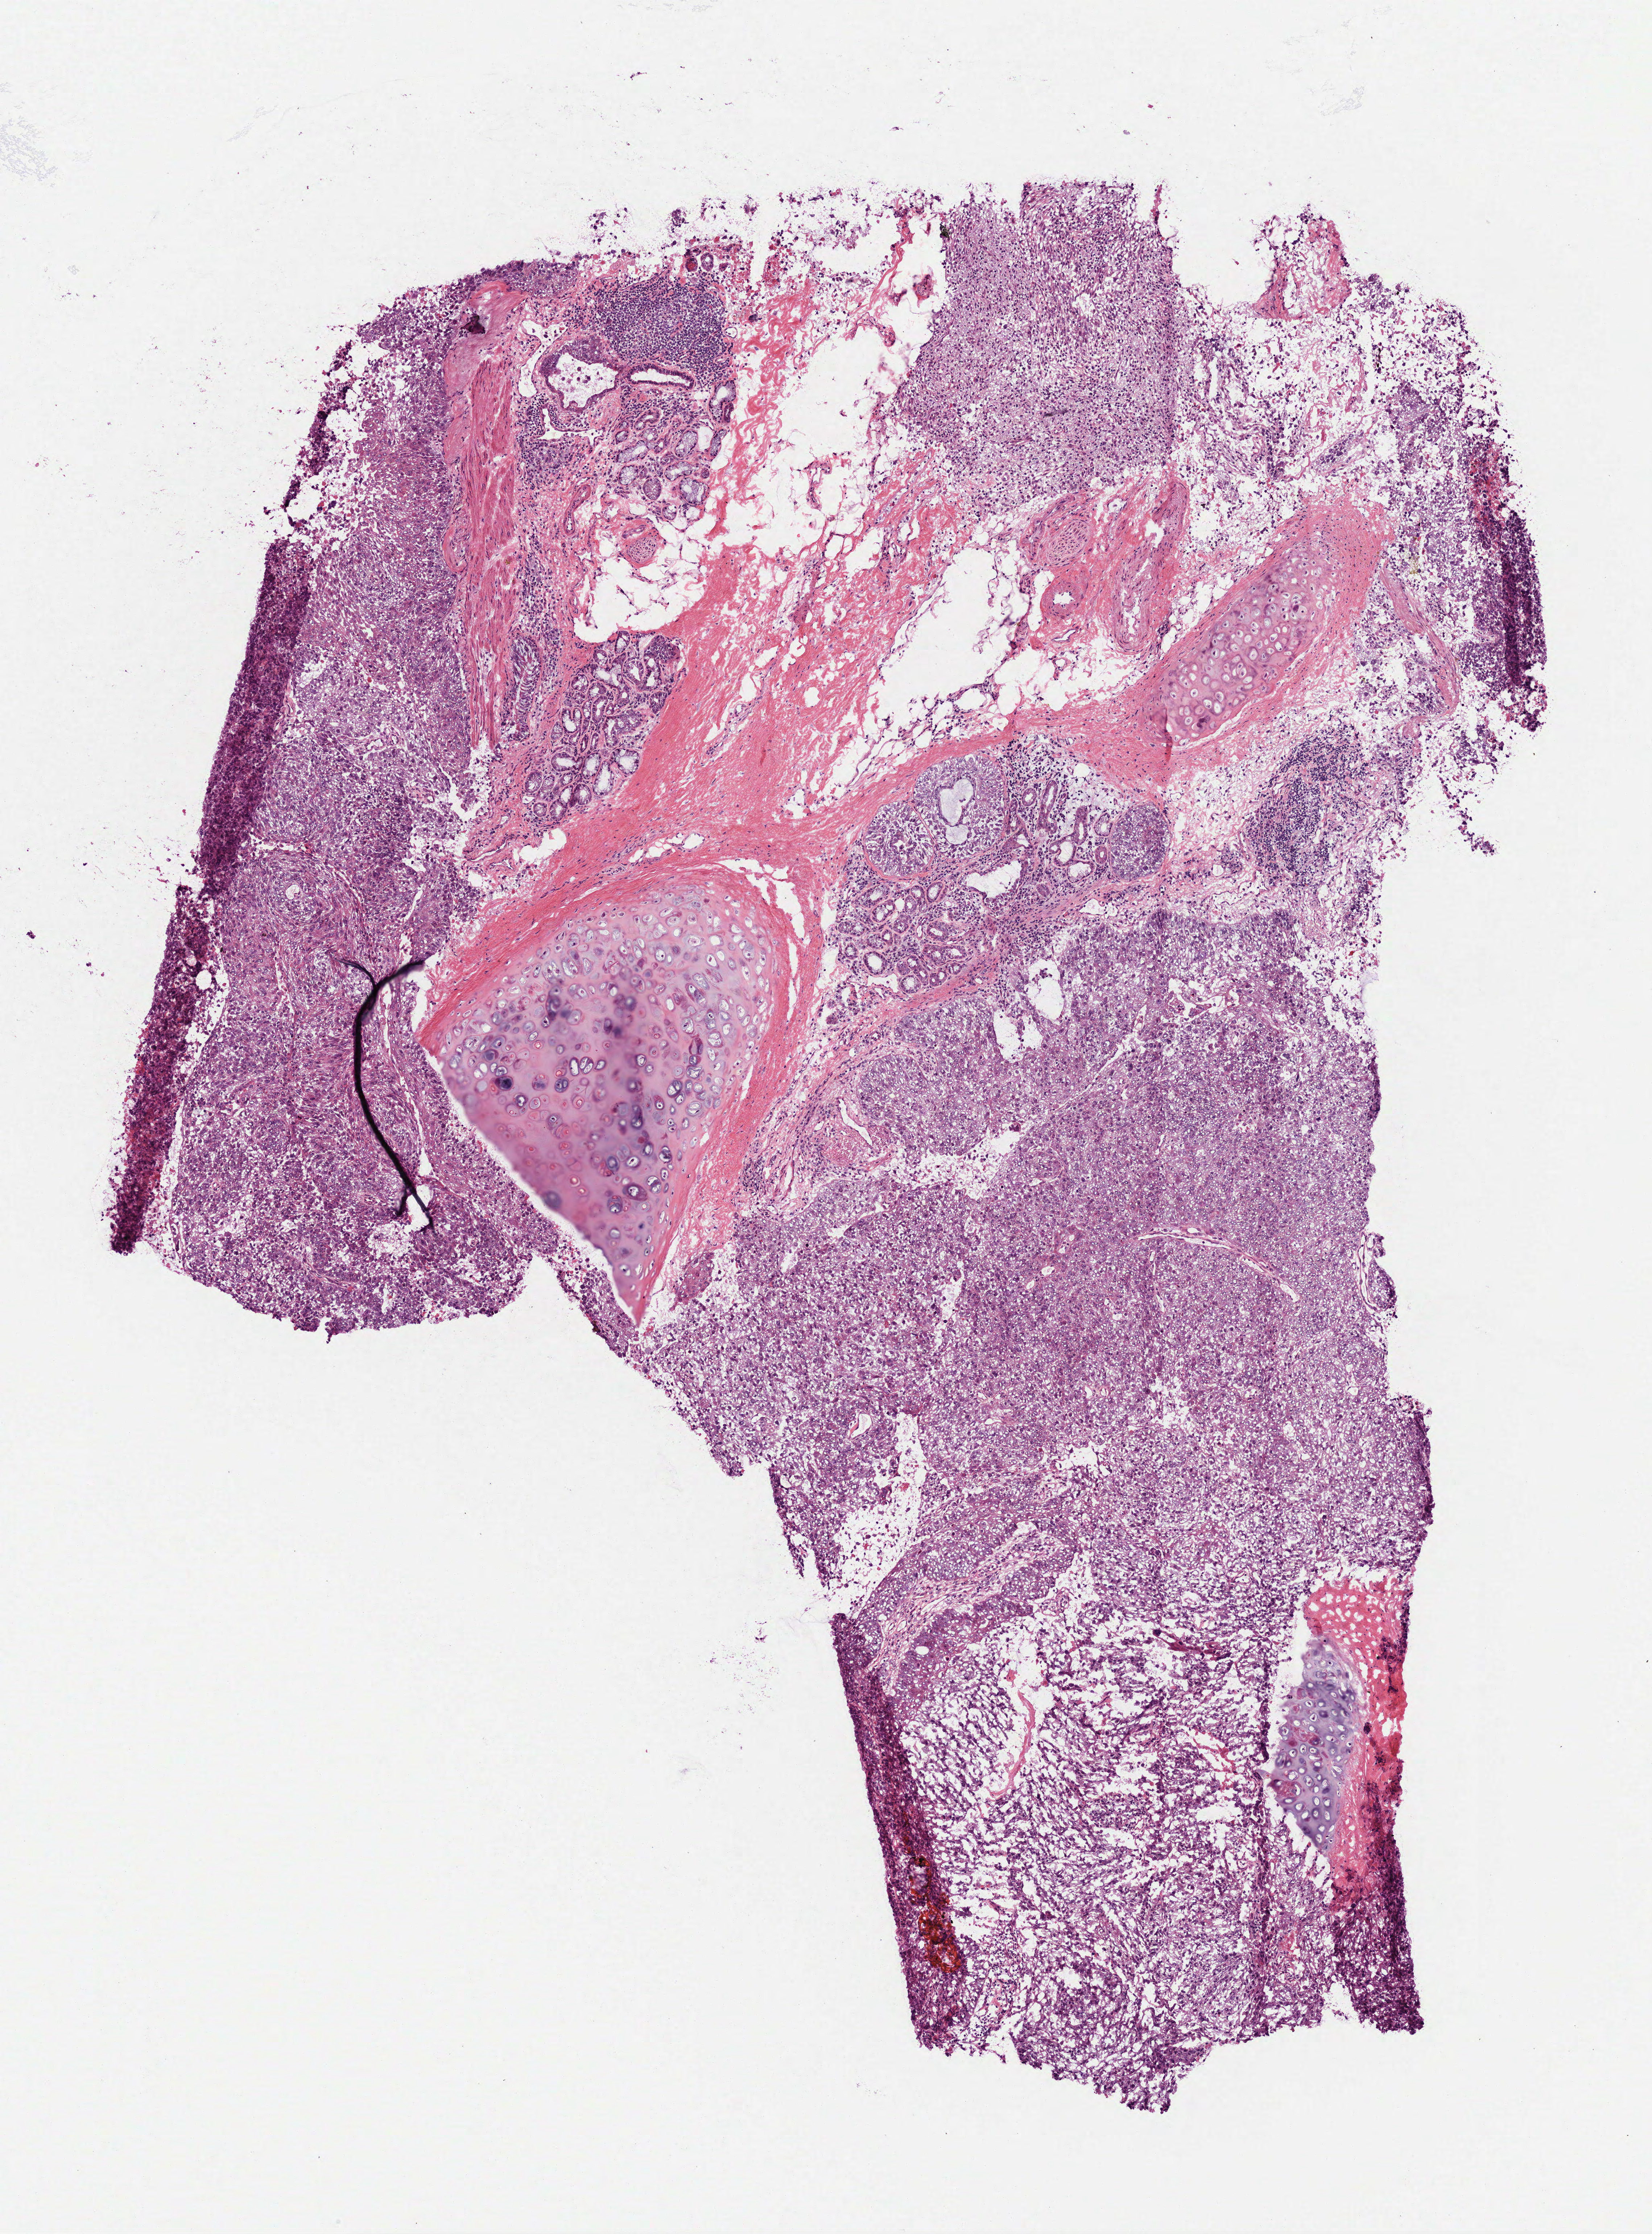
Digitized H&E-stained tissue section (whole slide) — low-resolution overview of the scanned area, about 4.6 x 6.2 mm (acquisition: 40x scan), frozen section from the top of the tissue portion, lung, primary tumour sample. Male patient; age at initial diagnosis 64 years. Composition of this section per pathologist review: tumour cells 62%, tumour nuclei 75%, normal cells 18%, stromal cells 10%, necrosis 10%.
AJCC pathologic stage: IB. Histologic diagnosis: Squamous cell carcinoma, NOS. Laterality: left.